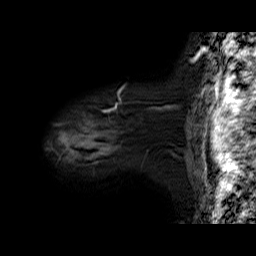
Breast MRI (dynamic contrast-enhanced), one sagittal slice; position 56 of 60 along the scan axis; dynamic contrast-enhanced series, time point 2 of 6 at this slice position (early post-contrast); 1.5 T; TE 6.3 ms, TR 32.9 ms; 4 mm slice thickness; 256 × 256 image matrix, field of view 200 × 200 mm. Female patient. Case-level facts recorded for this patient, not image findings: setting: breast cancer imaged before/during neoadjuvant chemotherapy; receptor status: HER2-positive.
Structures marked on this image (semi-automatically segmented with operator editing):
- analysis volume of interest (the breast-tissue region the enhancement analysis was run in; not a lesion): bounding box [x1, y1, x2, y2] px = [56, 90, 178, 167]
- tumour enhancement mask (voxels above the 100 % enhancement threshold inside the analysis volume of interest): [114, 108, 117, 111]